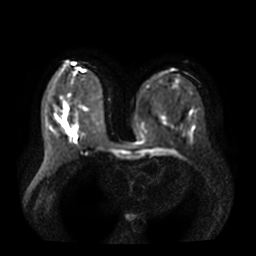
Breast MRI, one axial slice; slice 16 of 36 in the series (ordered by position); diffusion-weighted series; image 2 of 4 stored at this slice position (different b-values; order by instance number); 3 T; 5 mm slice thickness; 256 × 256 image matrix. Female patient.
Structures marked on this image (manually delineated by an expert):
- tumour on diffusion-weighted imaging: bounding box (x1, y1, x2, y2) in pixels: (69, 129, 75, 134)